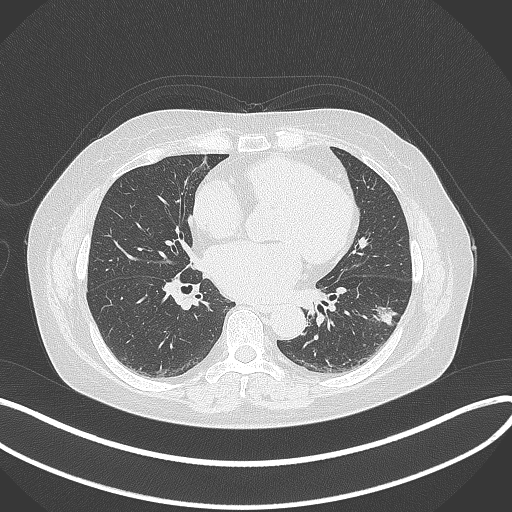
Chest CT, one axial slice; slice 161 of 373 in the series (ordered by position); reconstruction kernel B70f; 120 kVp; lung window (W 1500 / L -600 HU); 1 mm slice thickness; 512 × 512 image matrix. Female patient, age 67 years. Case-level facts recorded for this patient, not image findings: clinical TNM (as recorded): T1c N0 M0; histopathological grade: G2.
Outlined on this slice (rectangle marked by the reading radiologist):
- lung tumour (recorded histology: adenocarcinoma): bounding box (x1, y1, x2, y2) in pixels: (368, 297, 401, 334)